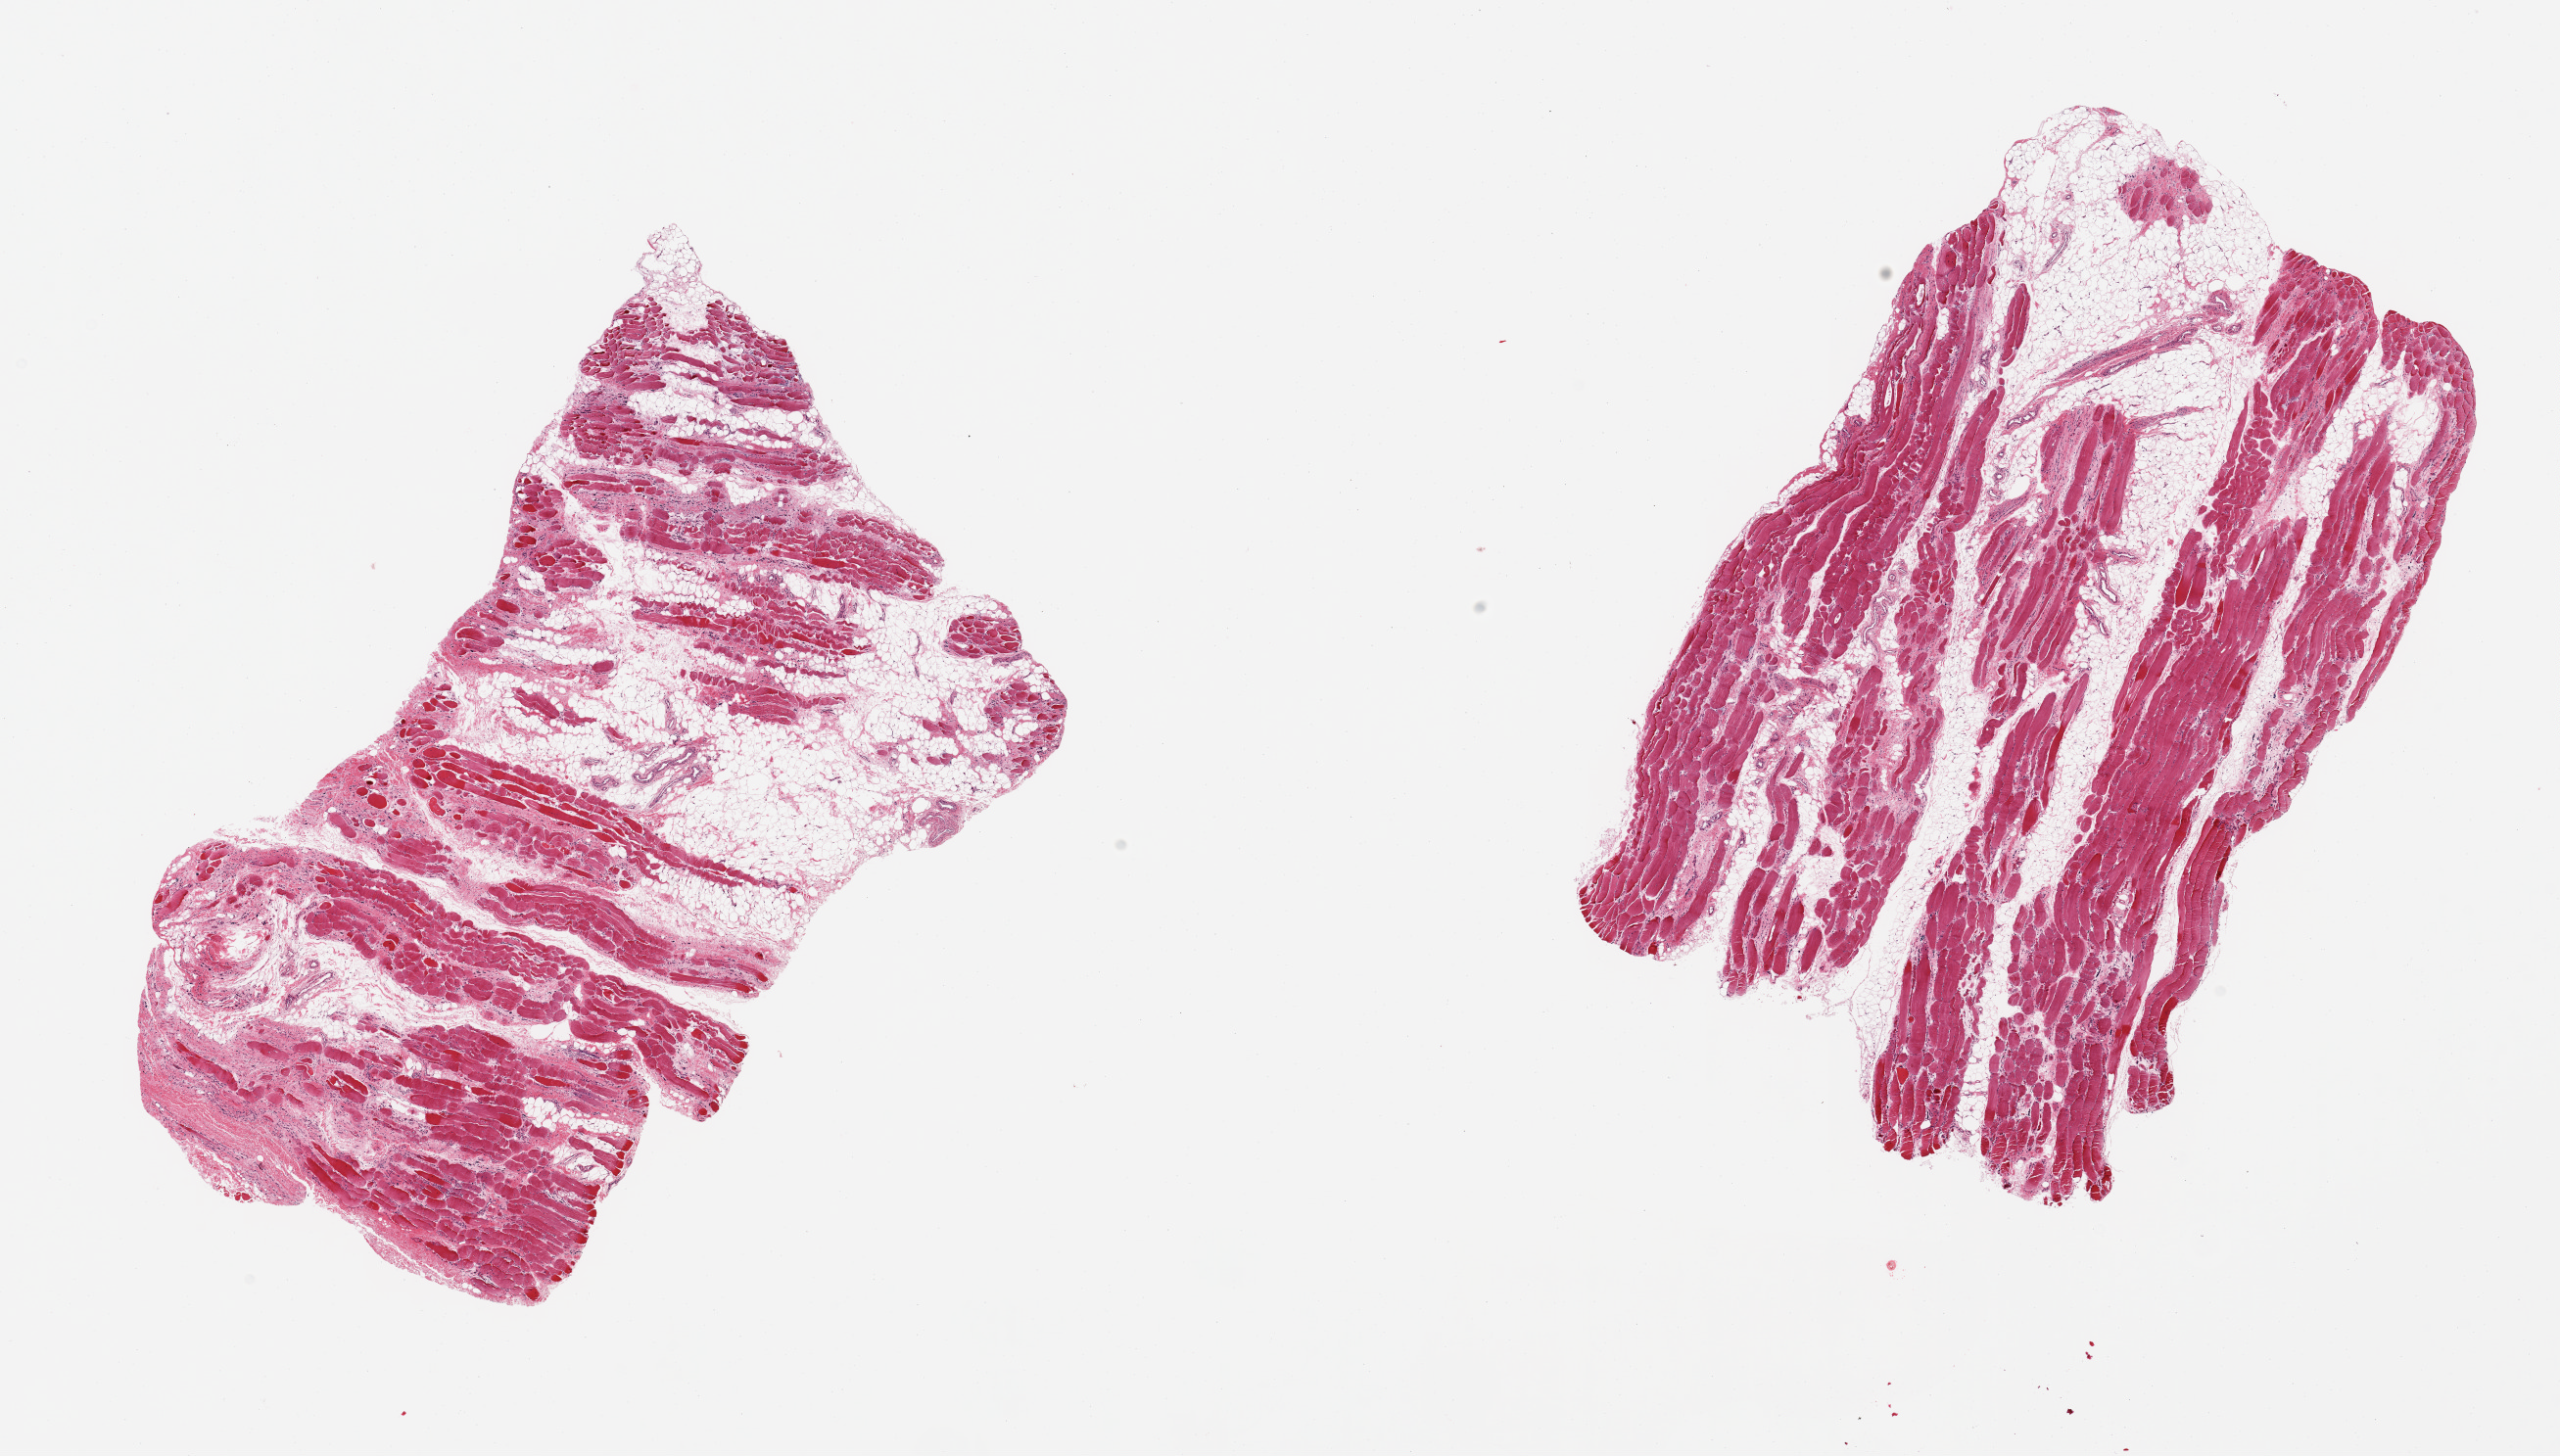
Haematoxylin and eosin whole-slide image — a low-resolution overview of the entire scanned area, about 20.7 x 11.8 mm (acquisition: 20x scan), PAXgene-fixed paraffin-embedded (PFPE) section, sampled site (target tissue): skeletal muscle, tissue donor sample. Donor: male.
Reviewer comment on this tissue sample: 2 pieces; severe atrophy and fatty replacement up to 50%.